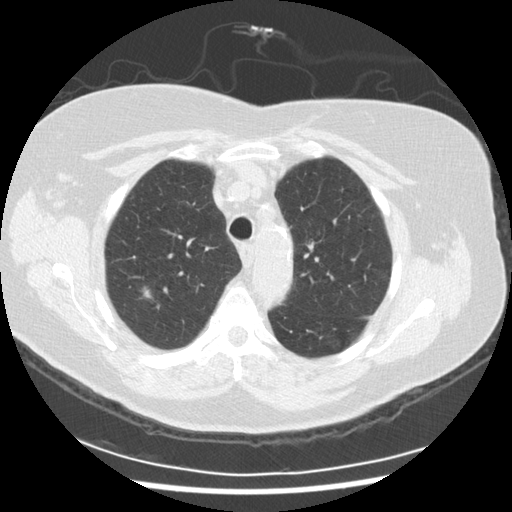
Low-dose screening chest CT, one axial slice; slice 203 of 254 in the series (ordered by position); 120 kVp; lung window (W 1500 / L -600 HU); 512 × 512 image matrix, field of view 360 × 360 mm.
Outlined on this slice (expert manual segmentation):
- lesion 1 (tumor, upper lobe of right lung): bounding box (x1, y1, x2, y2) in pixels: (143, 287, 152, 298)